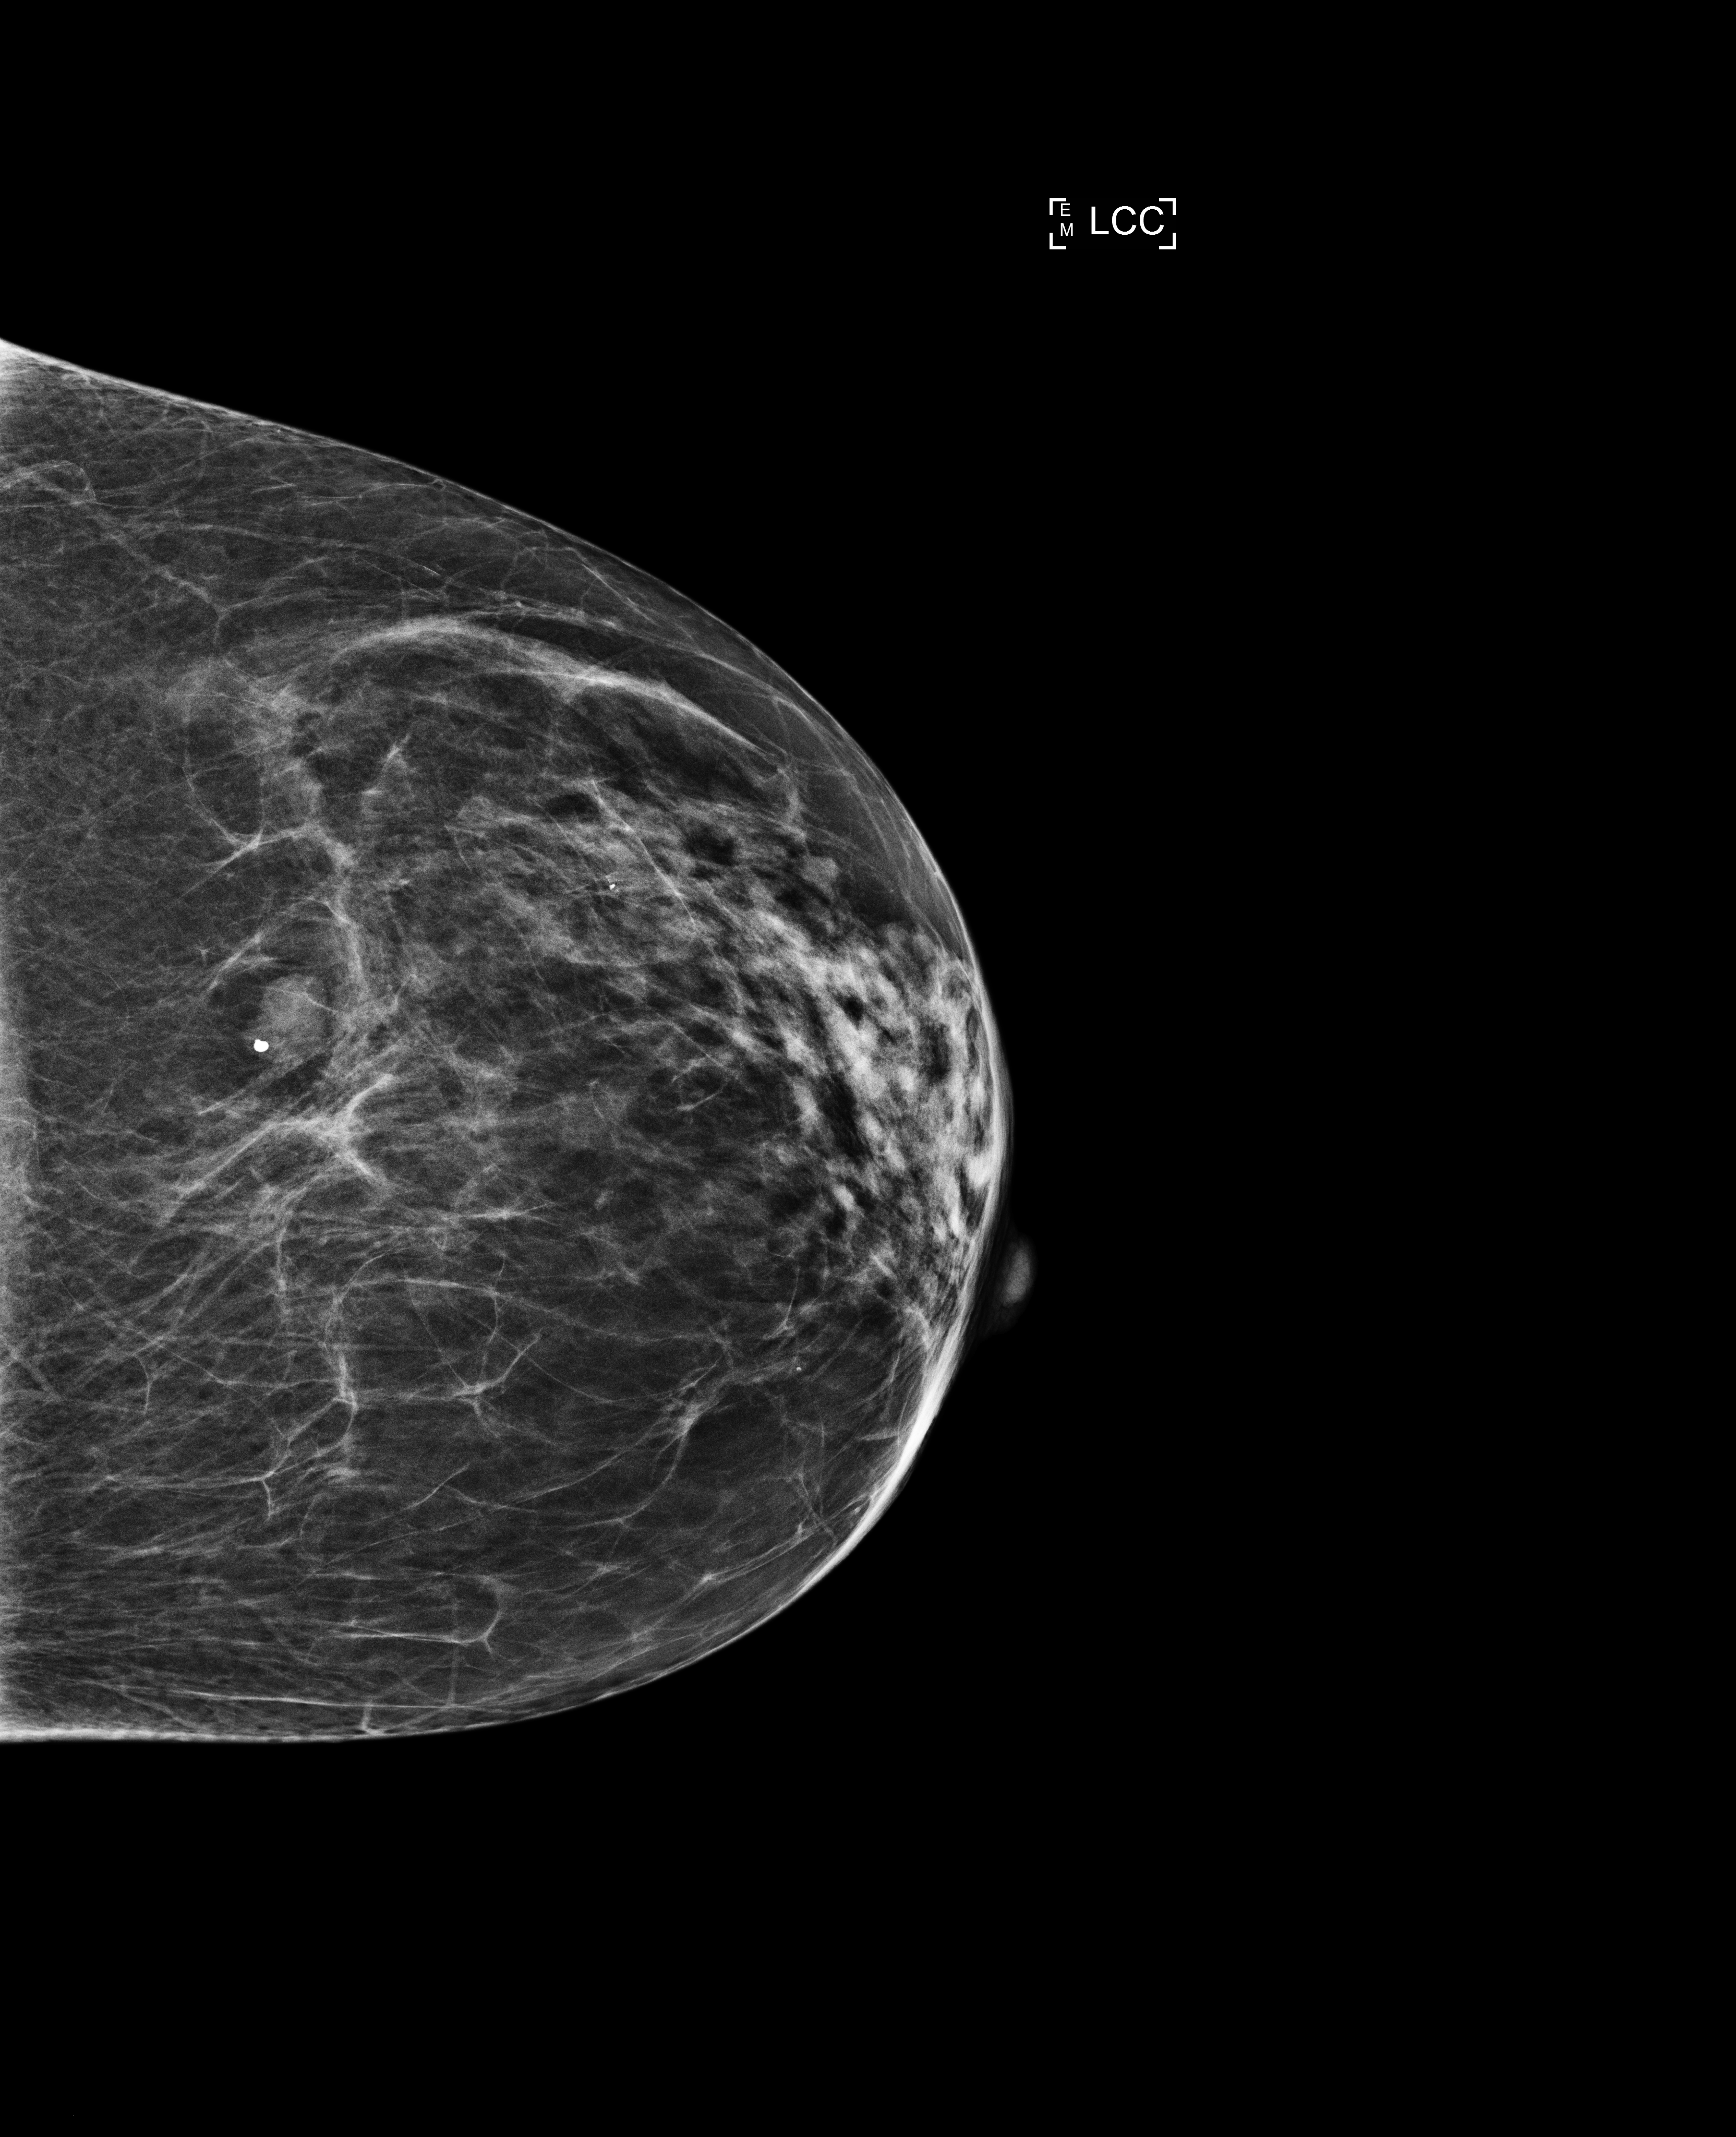
Annual screening mammography examination, system: Selenia Dimensions. Patient aged 65 years (female).
Image type: full-field digital mammogram. Breast: left. Projection: cranio-caudal projection.